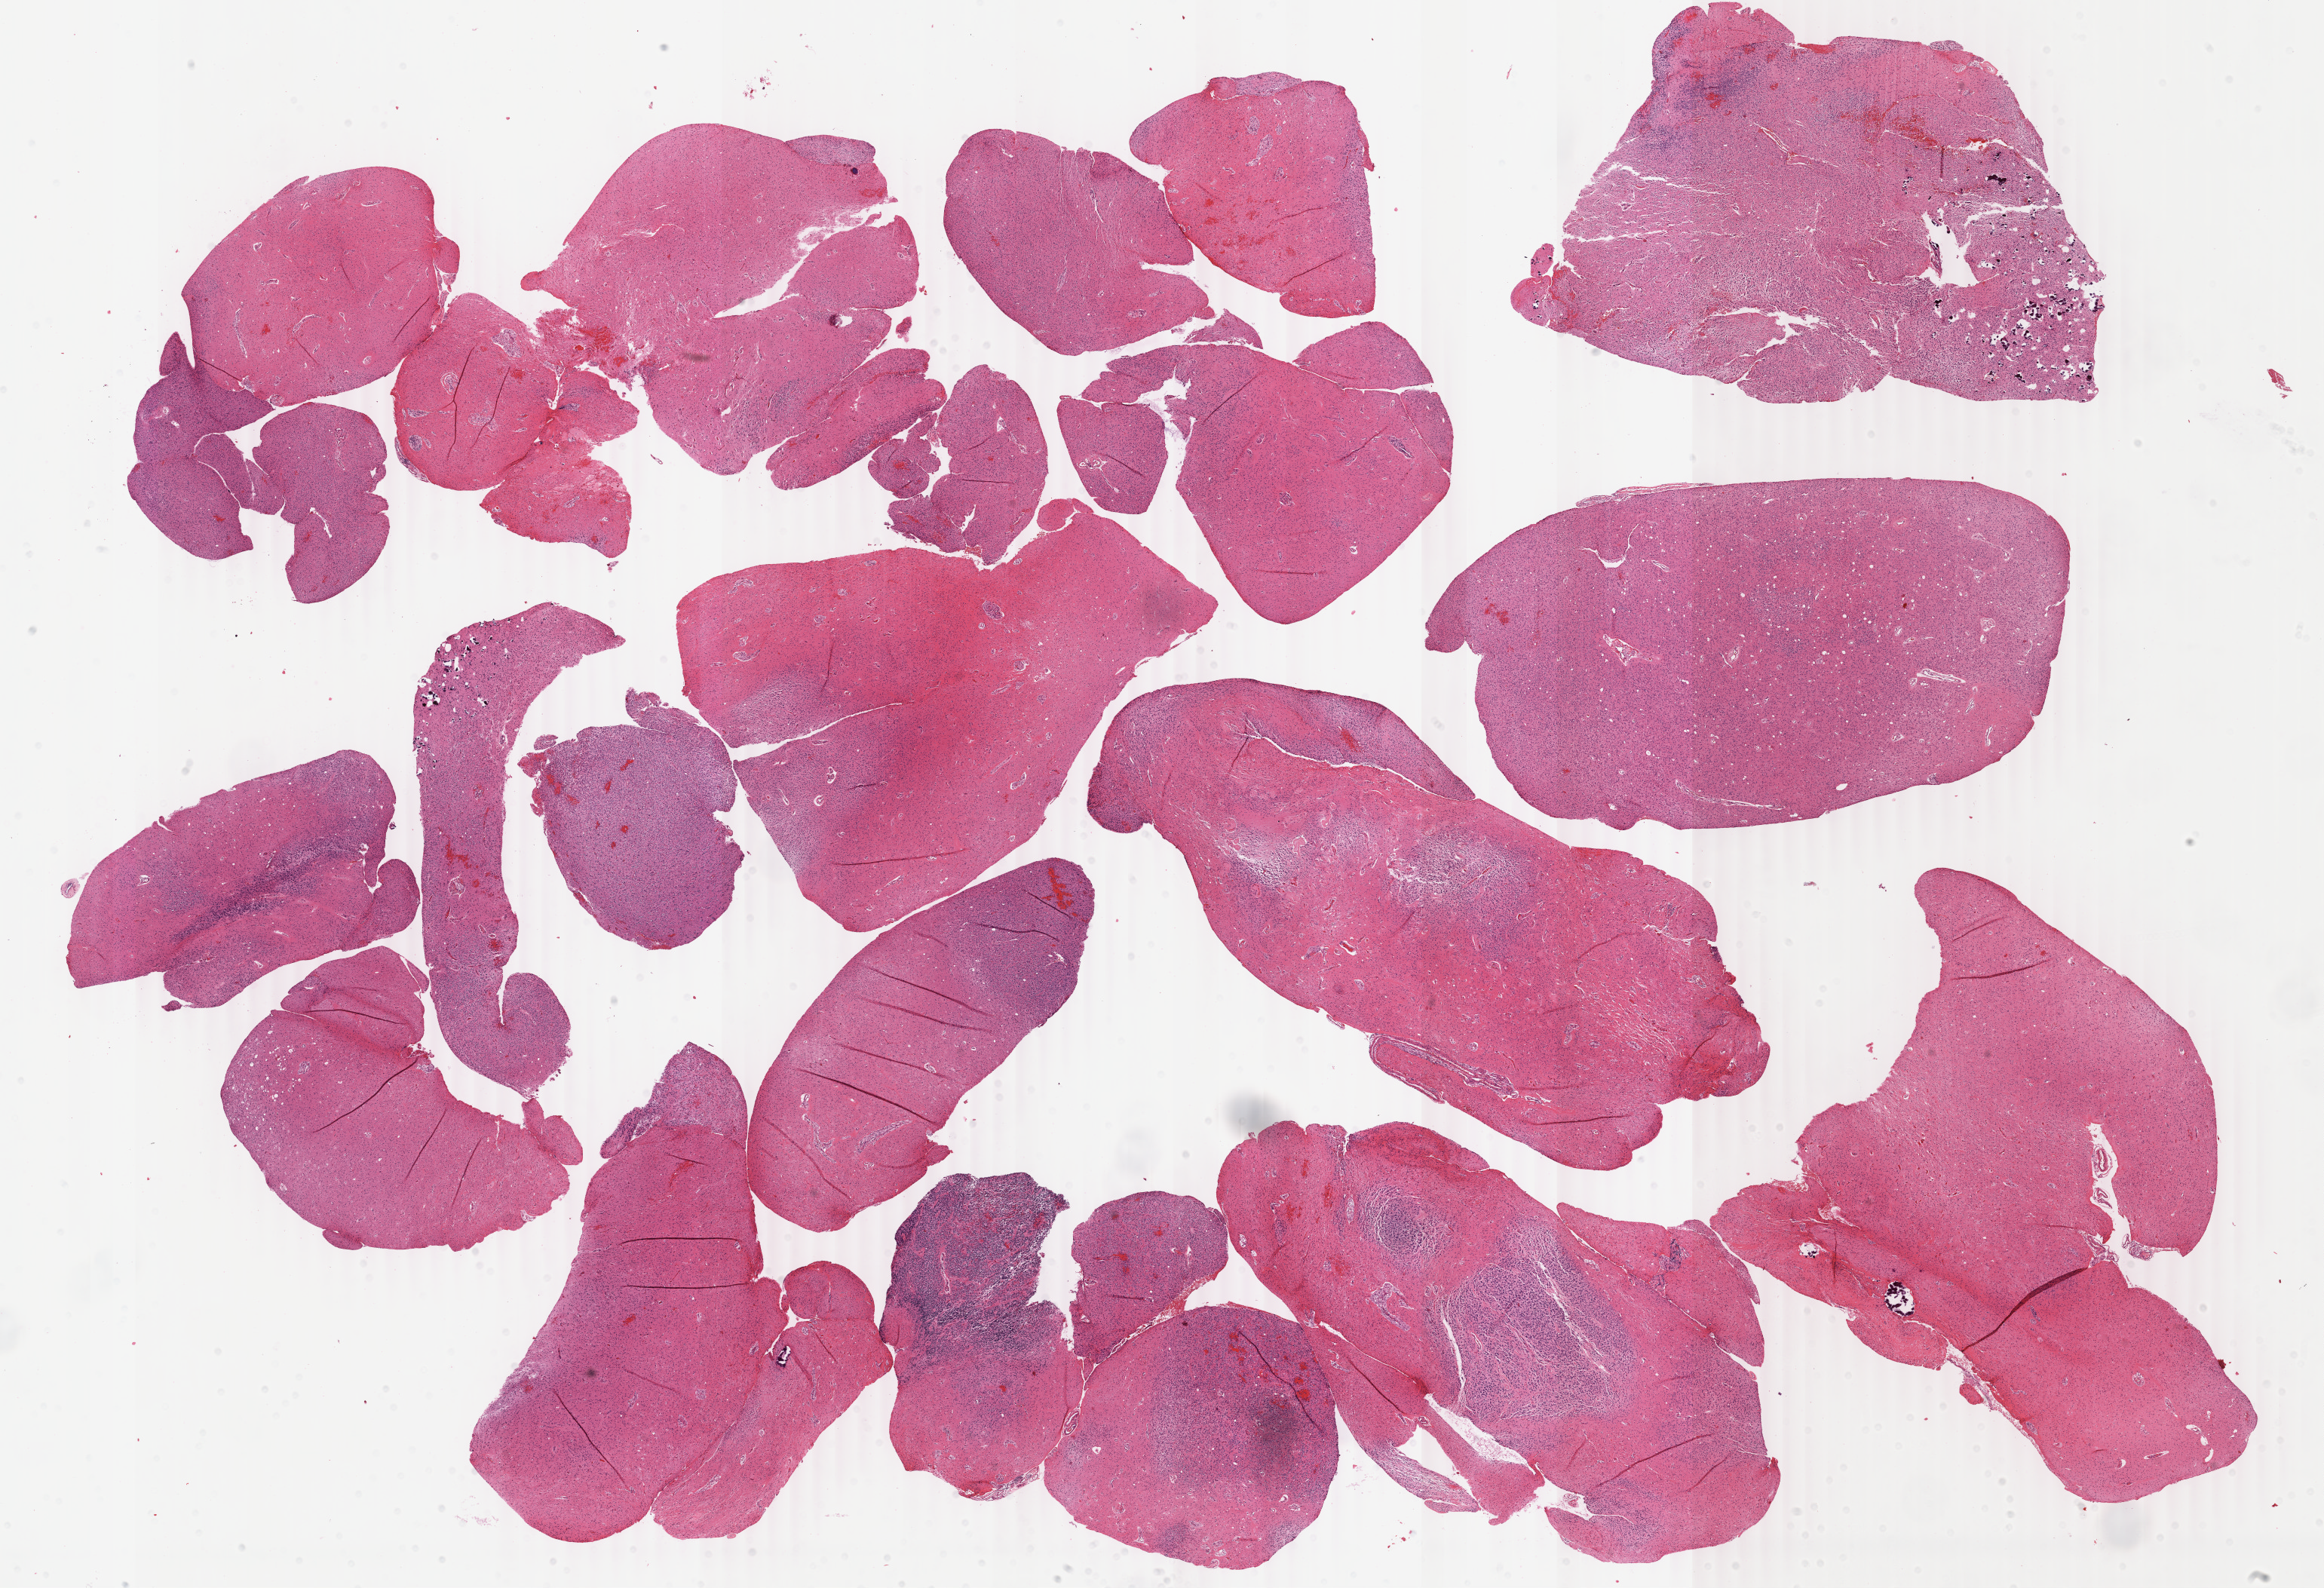
H&E whole-slide image — shown as a low-resolution overview of the whole scanned area (about 24.5 x 16.7 mm, slide scanned at 40x), formalin-fixed paraffin-embedded (FFPE) diagnostic section, sample: primary tumour, brain. Male, age 49 years at initial diagnosis. Histologic grade: G2 (moderately differentiated).
* diagnosis: Oligodendroglioma, NOS (cerebrum)
* laterality: left